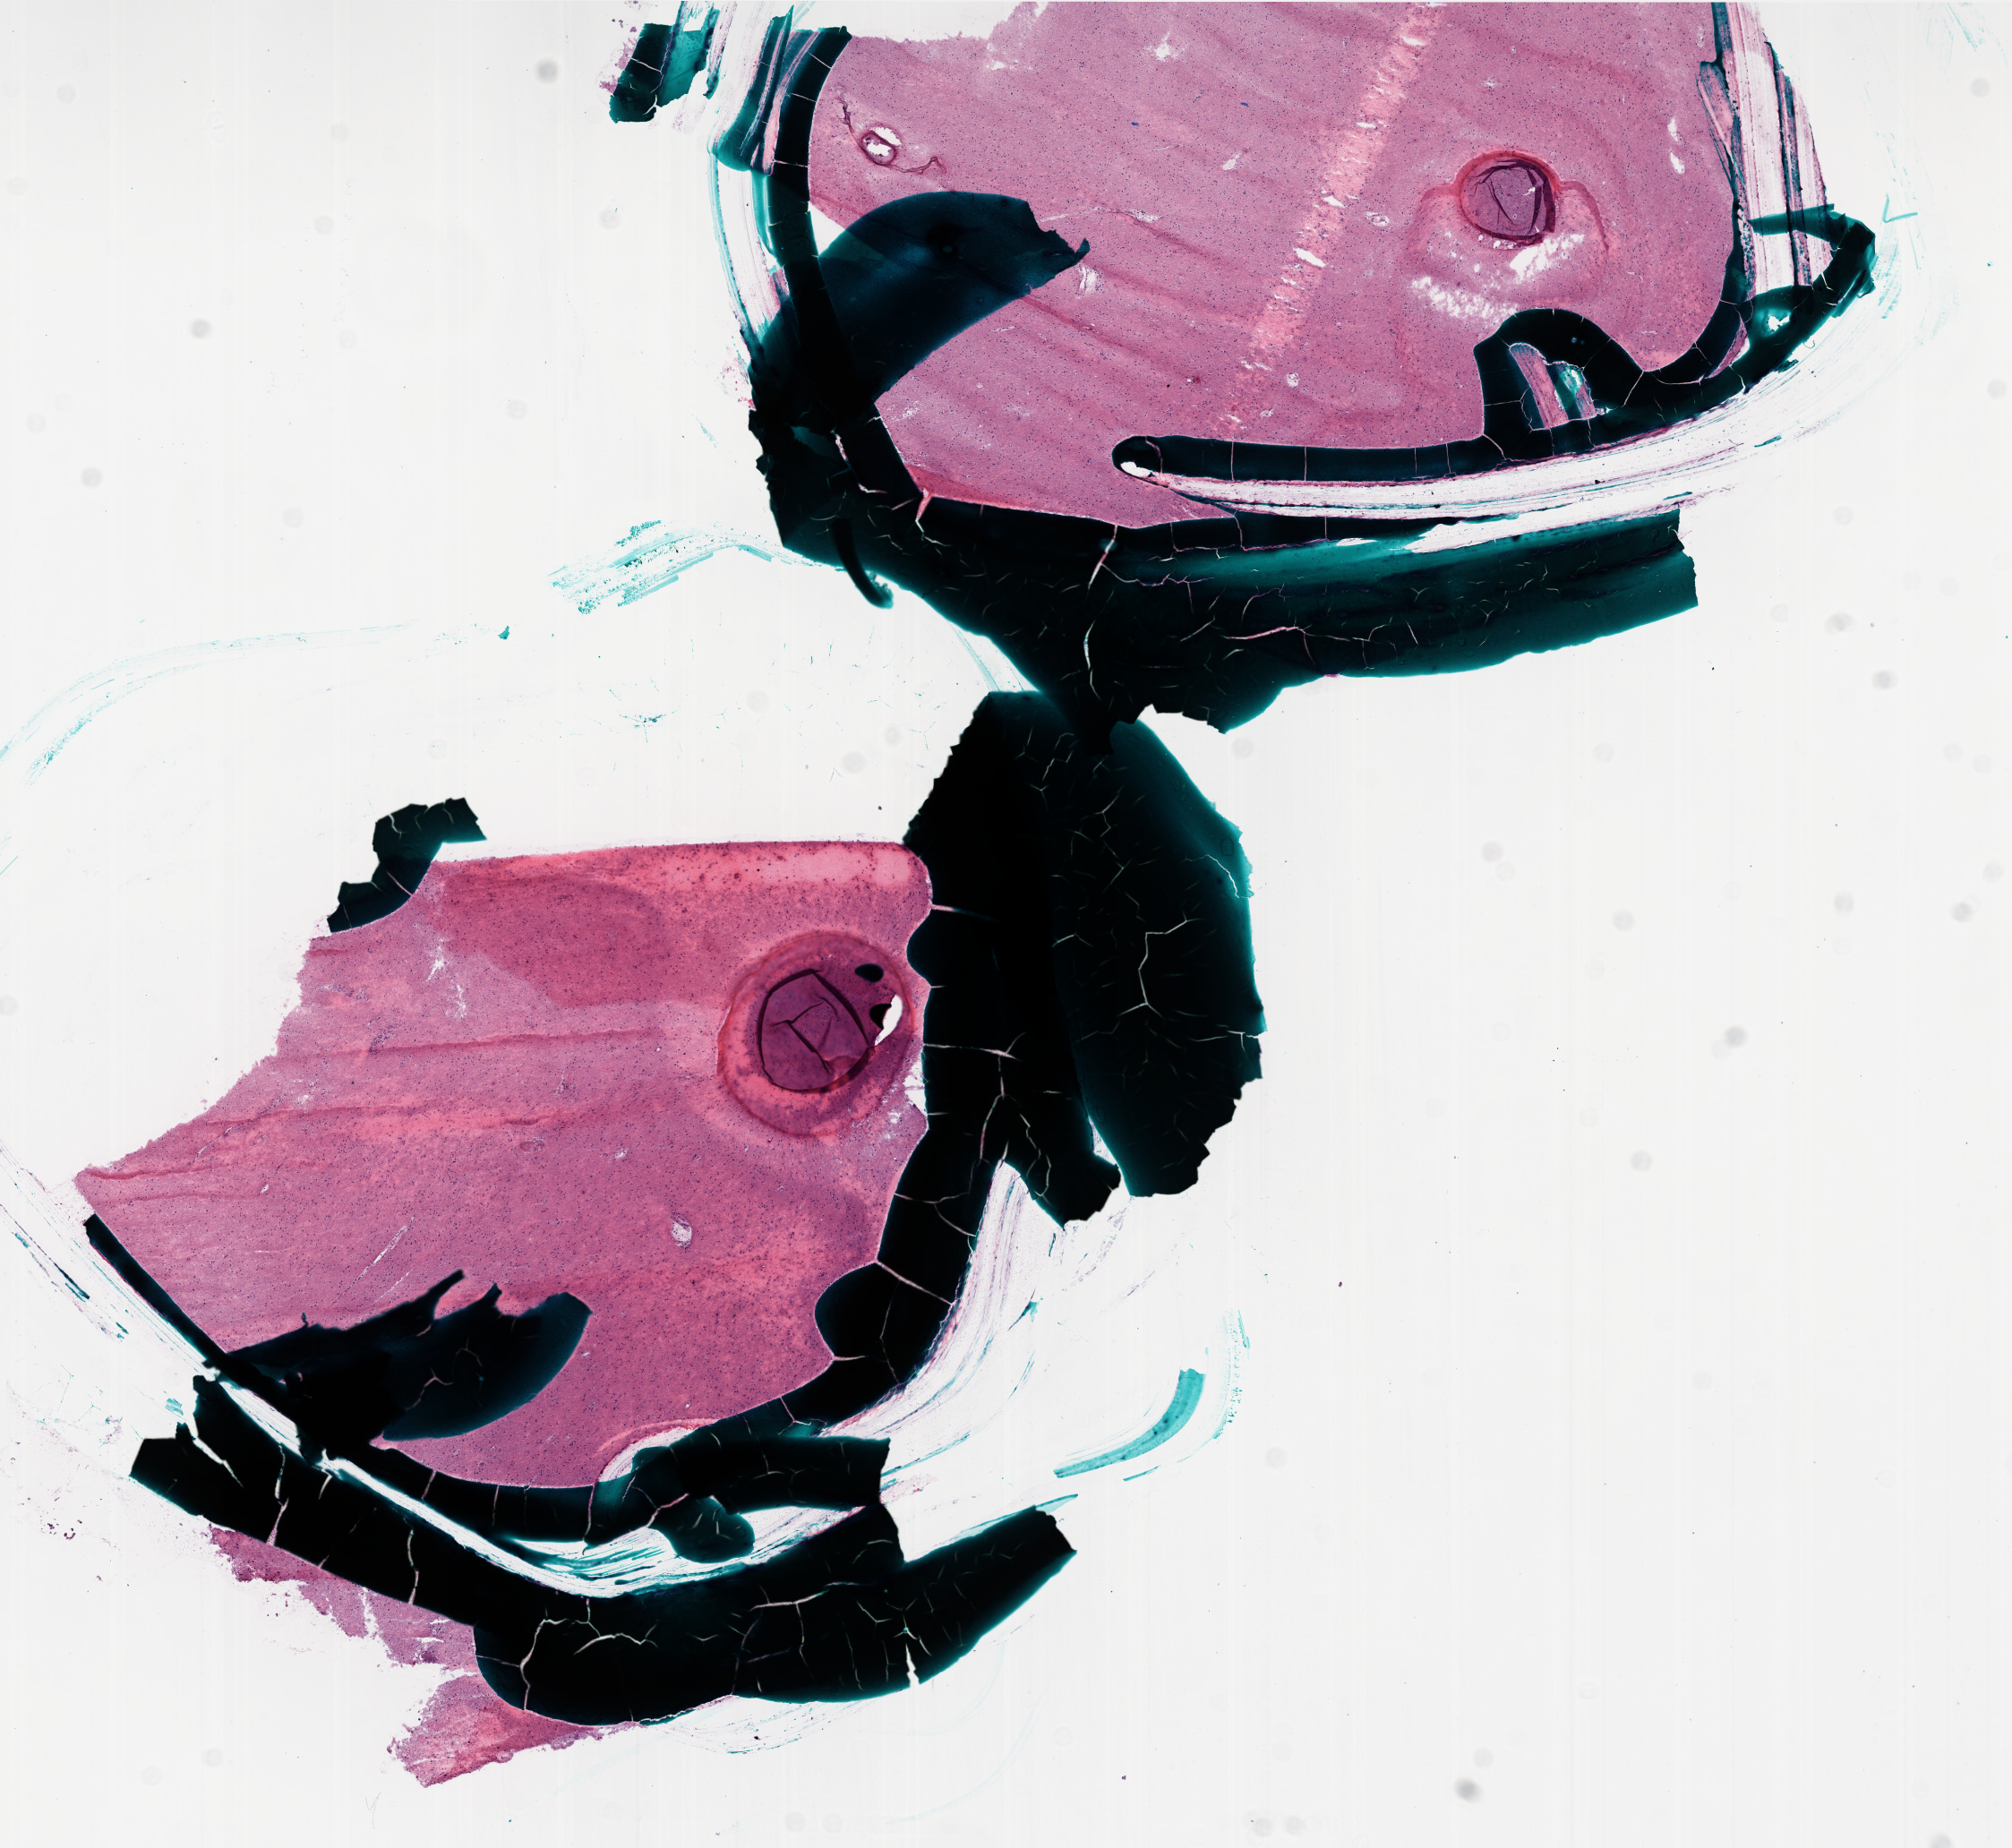
Whole-slide histology image, H&E — shown as a low-resolution overview of the whole scanned area (about 9.0 x 8.3 mm); frozen section; brain, primary tumour sample. Male patient; age at initial diagnosis 57 years. Slide review estimates, as recorded: tumour cells 0%, tumour nuclei 10%, normal cells 0%, stromal cells 100%, necrosis 0%.
• histologic diagnosis: Glioblastoma